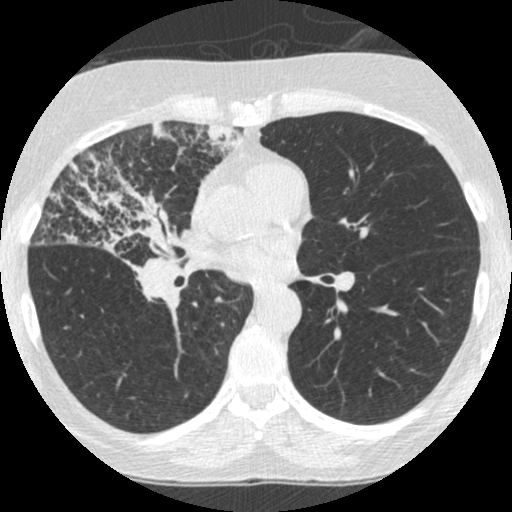
Low-dose screening chest CT, one axial slice; position 137 of 253 along the scan axis; reconstruction kernel STANDARD; lung window (W 1500 / L -600 HU); 512 × 512 image matrix, field of view 294 × 294 mm.
Structures marked on this image (manually delineated by an expert):
- lesion 2 (tumor, hilum of right lung): bounding box <35,153,191,272> (left, top, right, bottom; pixels)
- lesion 3 (tumor, upper lobe of right lung): <152,123,178,145>
- lesion 4 (tumor, upper lobe of right lung): <205,123,247,160>